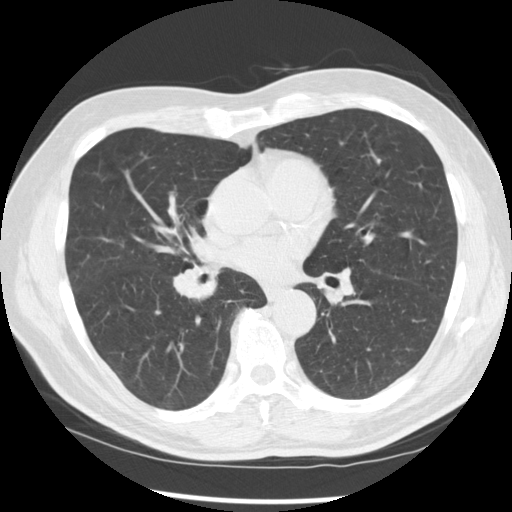
Low-dose screening chest CT, one axial slice. Position 143 of 277 along the scan axis. Lung window (W 1500 / L -600 HU). 512 × 512 image matrix.
Structures marked on this image (manually delineated by an expert):
- lesion 1 (tumor, middle lobe of right lung): bounding box (x1, y1, x2, y2) in pixels: (173, 266, 218, 302)